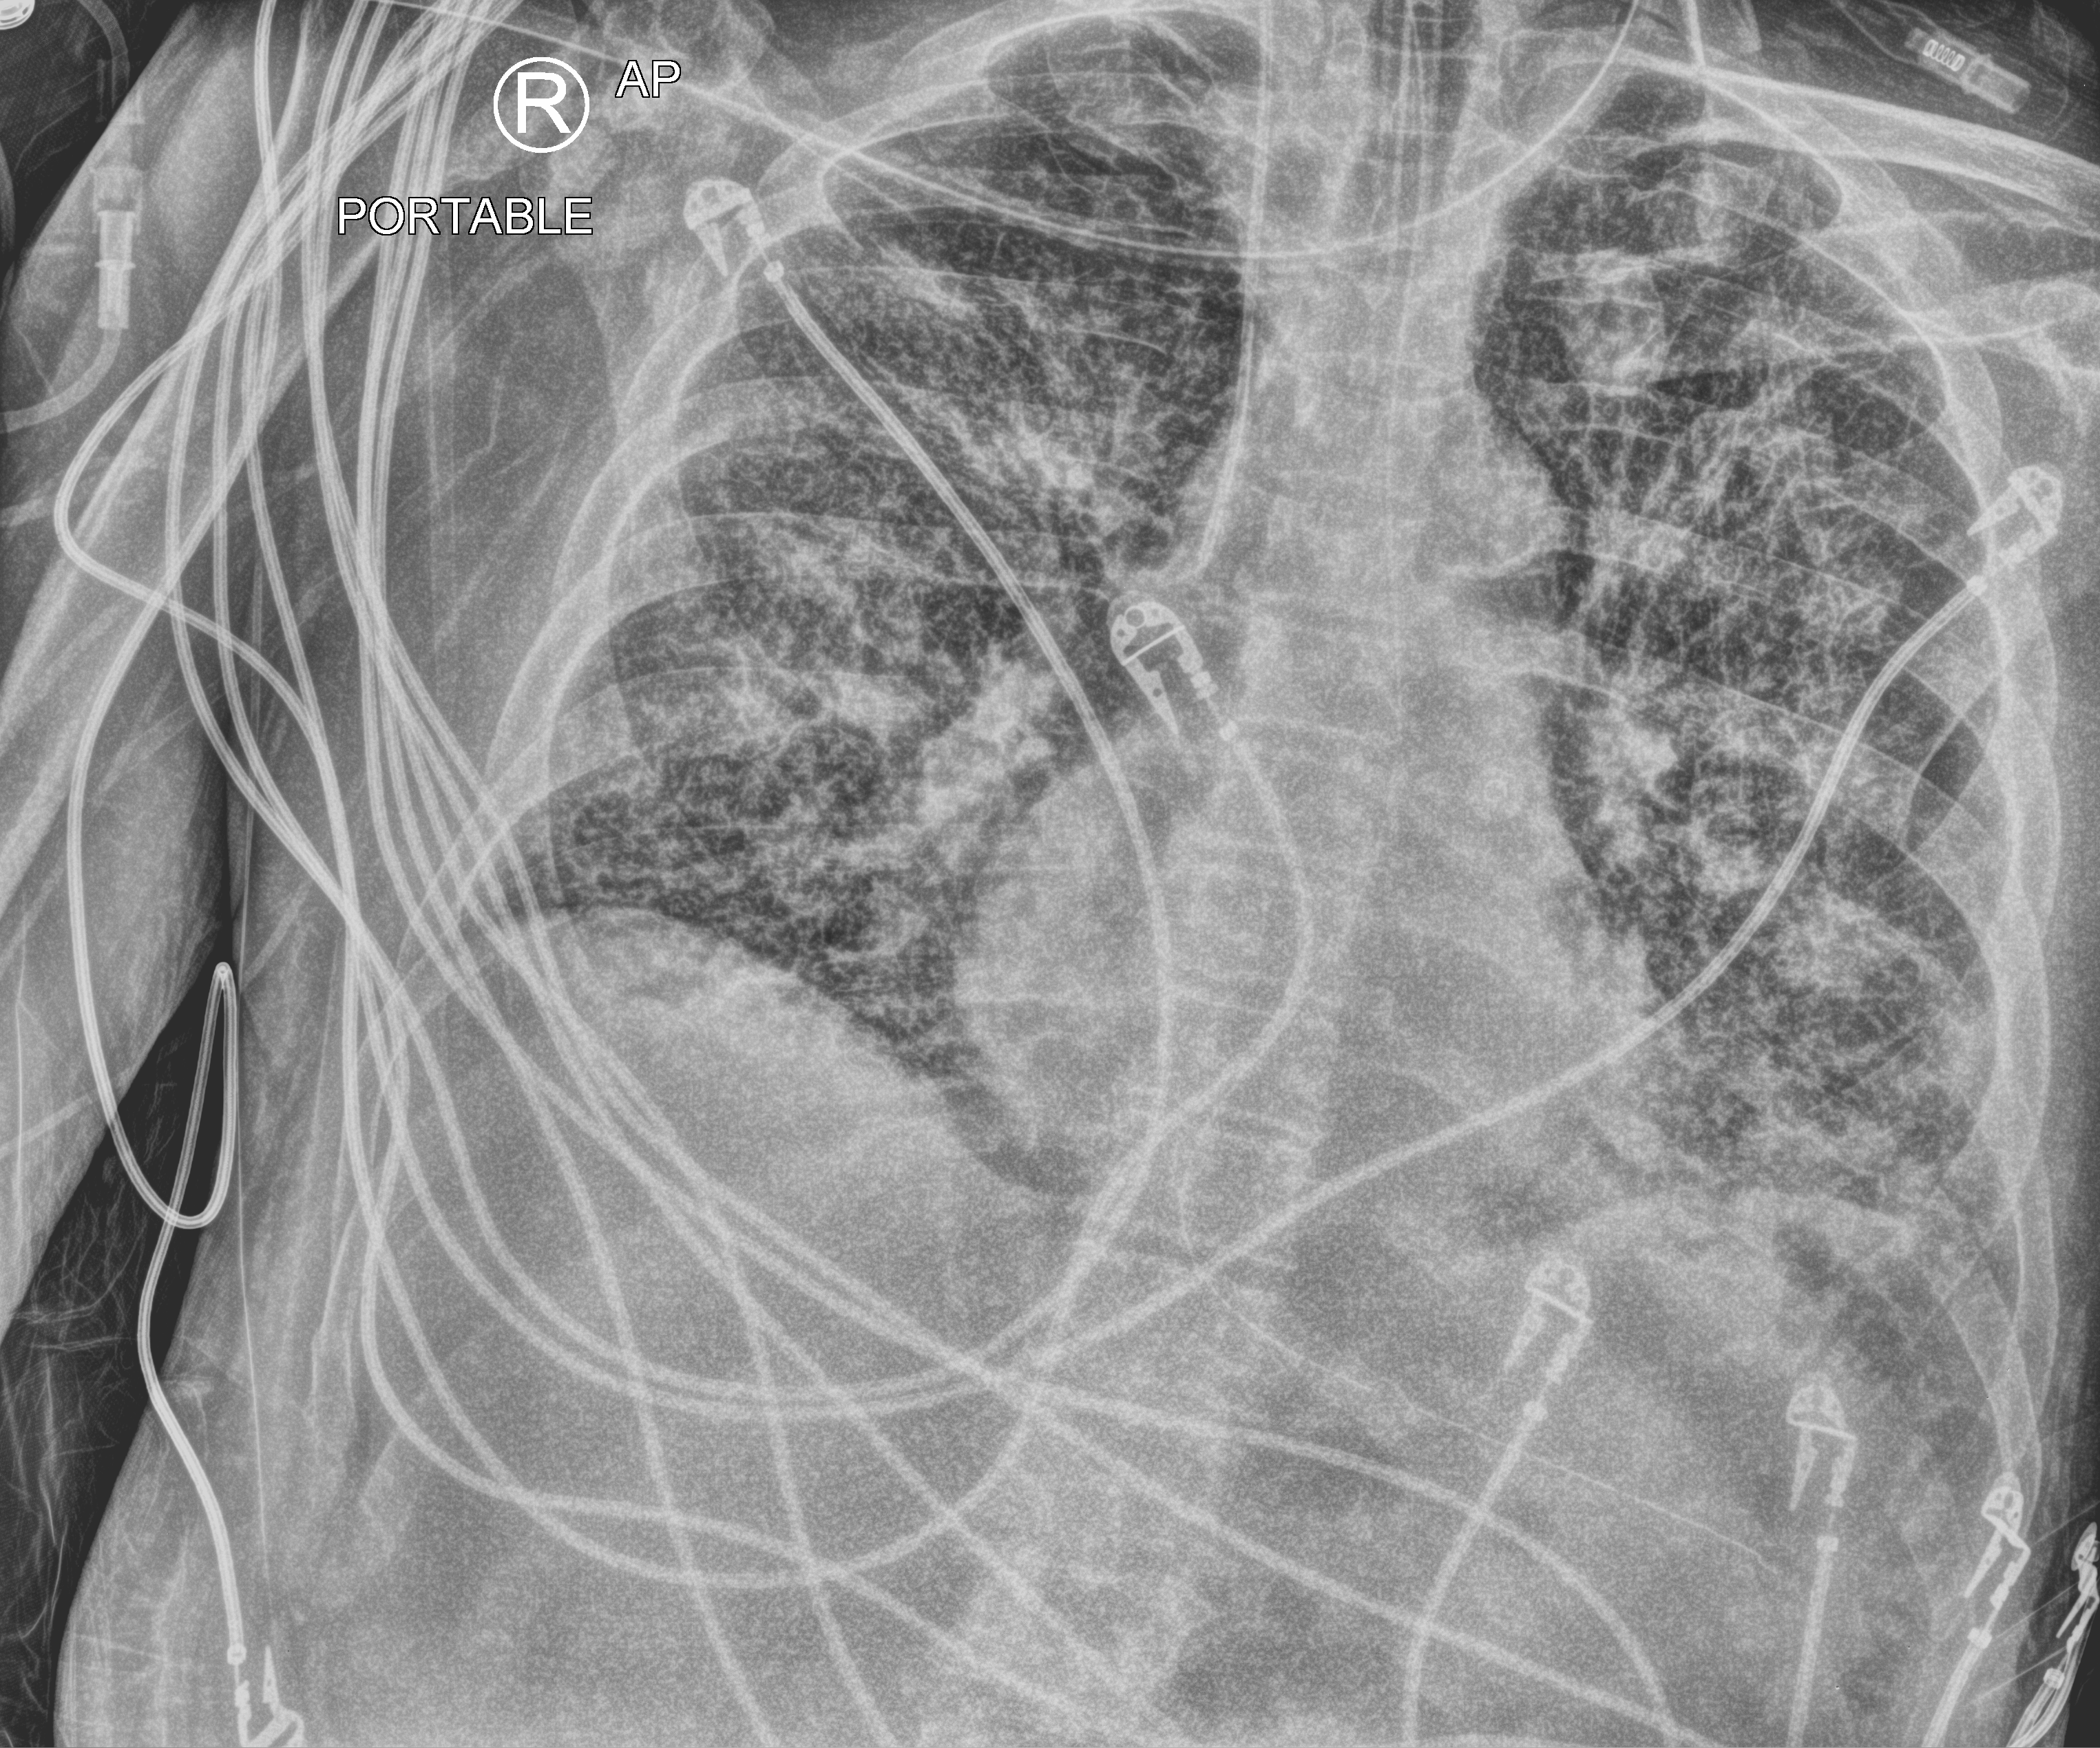
Bedside chest radiograph (computed radiography); anteroposterior (AP) projection. Patient hospitalised with COVID-19; male, aged 75–90 years.
Admission-level facts for this patient (not findings on this image; timing relative to this image not recorded):
- length of hospital stay: 13 days
- admitted to intensive care during this hospital stay: yes